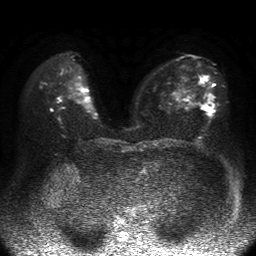
Breast MRI, one axial slice; slice 27 of 50 in the series (ordered by position); diffusion-weighted series; image 2 of 4 stored at this slice position (different b-values; order by instance number); 1.5 T; 4 mm slice thickness; 256 × 256 image matrix. Female patient.
Outlined on this slice (expert manual segmentation):
- tumour on diffusion-weighted imaging: box from (x=201, y=75) to (x=211, y=110) px